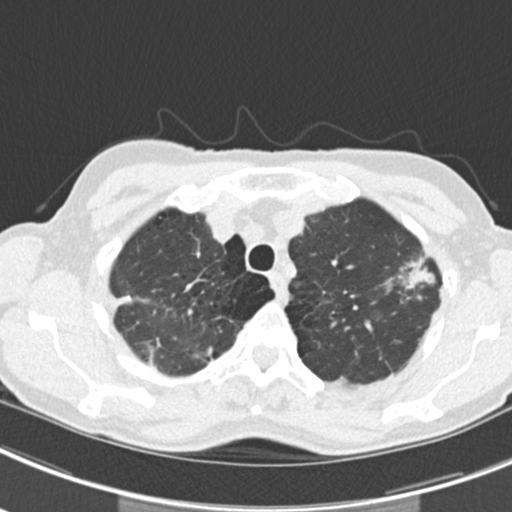
Low-dose screening chest CT, axial slice. Second screening round (one year after baseline). Lung window (W 1500 / L -600 HU). Standard (soft-tissue) reconstruction kernel (B30f). 512 × 512 image matrix. Female, age 63 years at enrolment. Current smoker at enrolment.
• Lesion marked by an expert reader, bounding box [x1, y1, x2, y2] px = [378, 245, 443, 306].
• The screening reader recorded 9 non-calcified nodules or masses ≥4 mm on this exam (left upper lobe, right upper lobe, left upper lobe, left lower lobe, right middle lobe, left lower lobe, left lower lobe, right lower lobe, right lower lobe); which of them this box marks is not recorded.
• Official screen result: positive, other.
• Participant outcome: lung cancer diagnosed 408 days after this screen — bronchiolo-alveolar adenocarcinoma, NOS, right upper lobe, right middle lobe, right lower lobe, left upper lobe, left lower lobe, moderately differentiated (G2), stage IV (AJCC 6th edition).